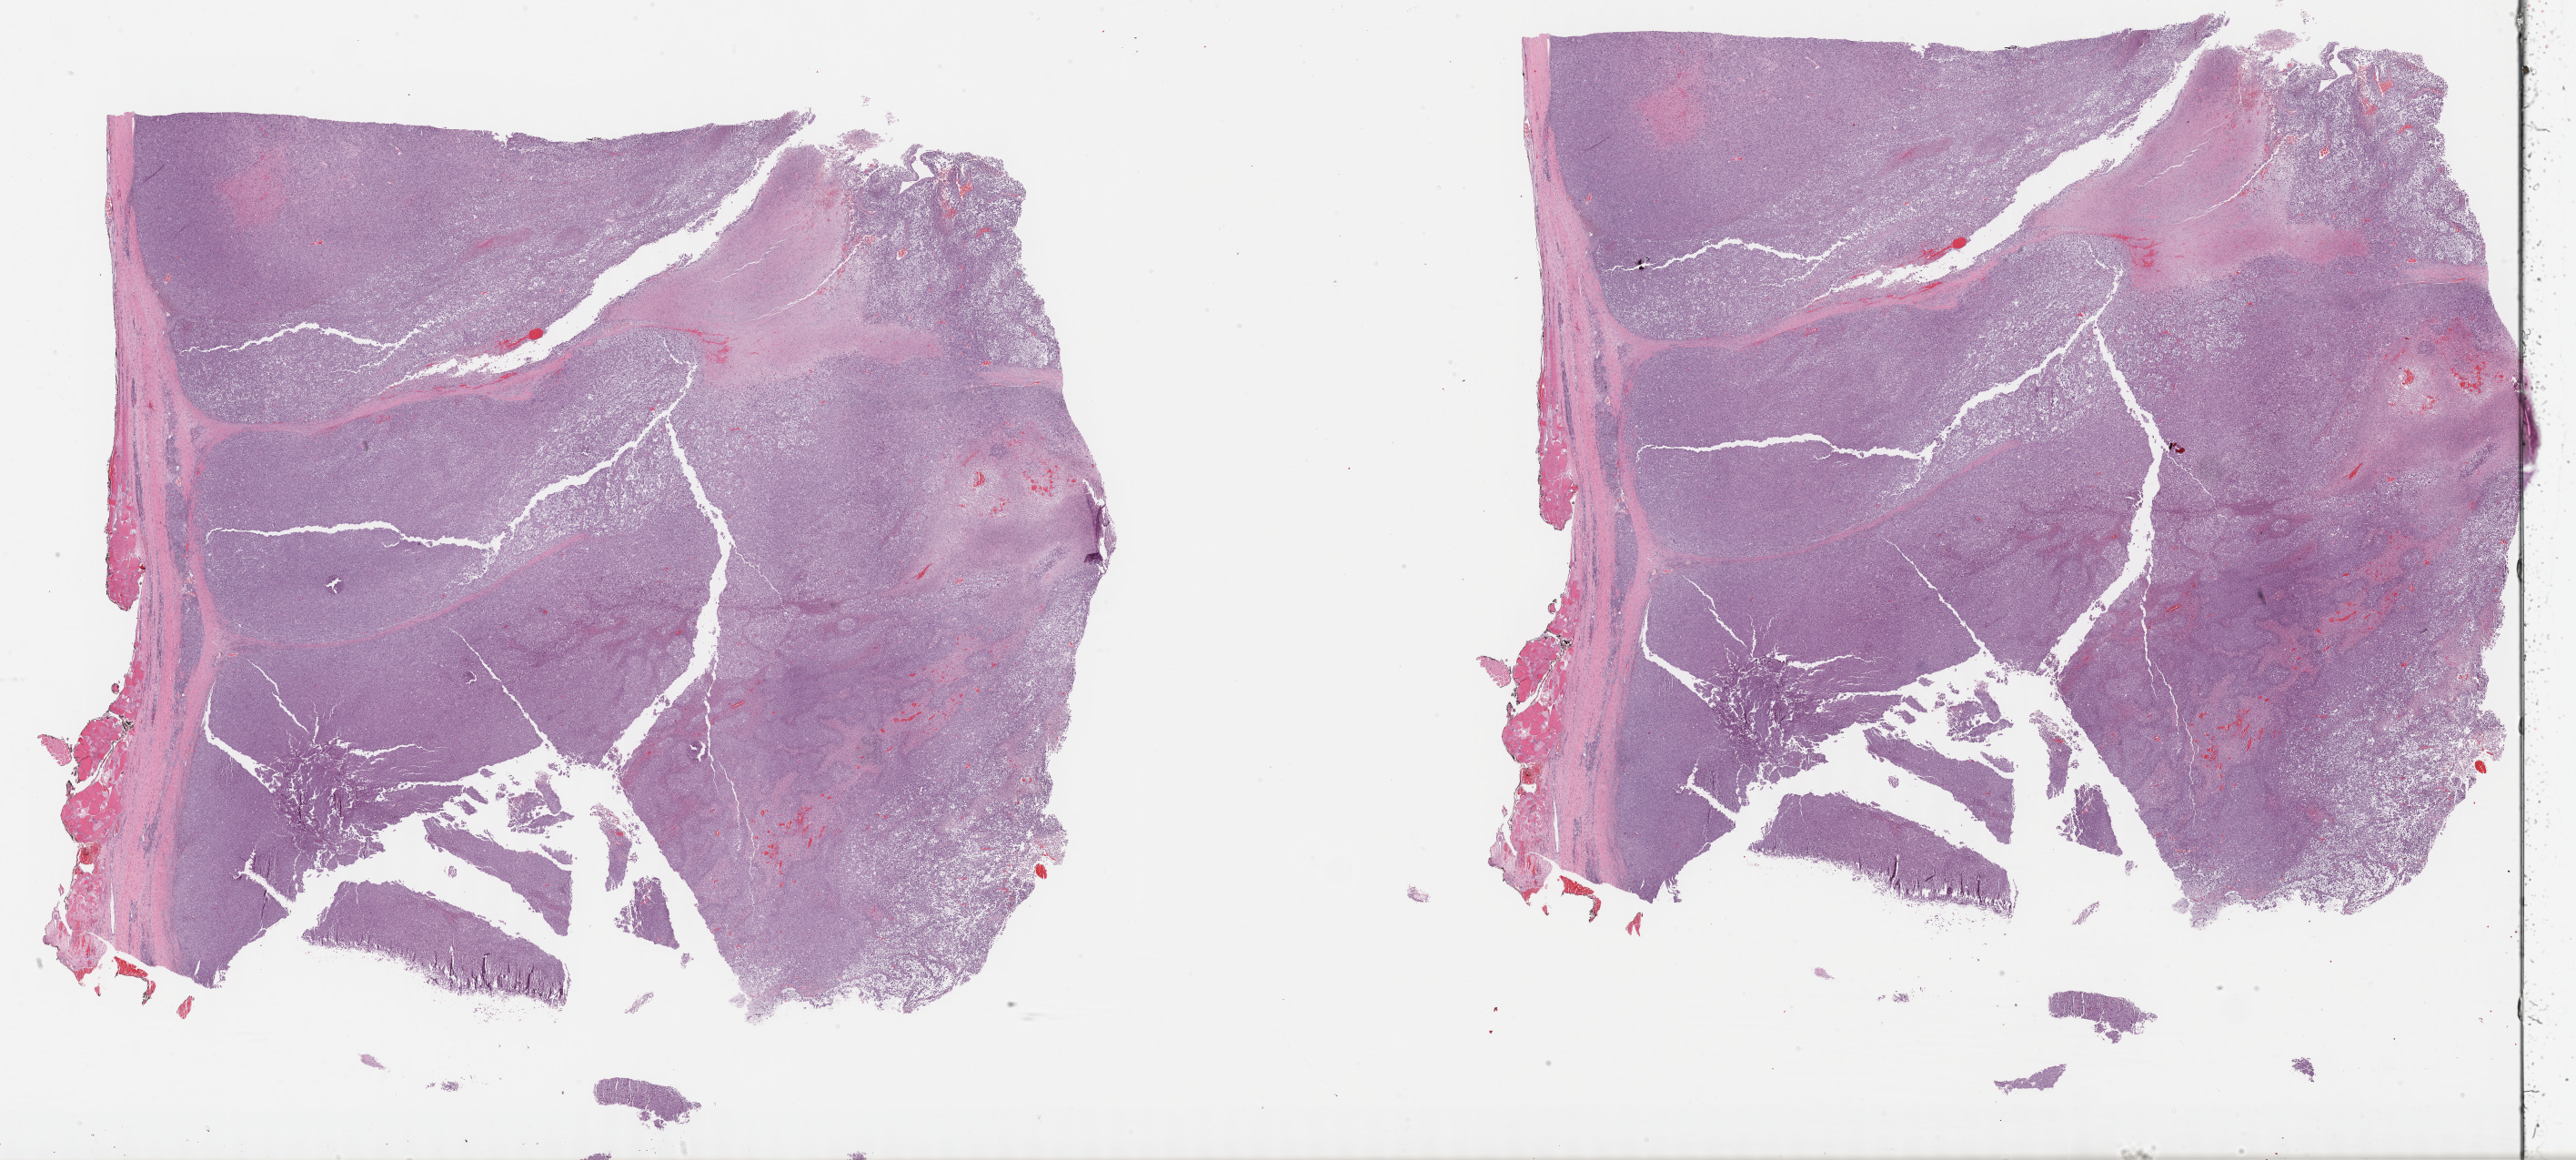
Whole-slide histology image, H&E-stained — low-resolution overview of the scanned area, about 45.8 x 20.6 mm (slide scanned at 40x). Formalin-fixed paraffin-embedded (FFPE) diagnostic section. Connective, subcutaneous and other soft tissues, primary tumour sample. Female, age 73 years at initial diagnosis.
• histologic diagnosis: Undifferentiated sarcoma